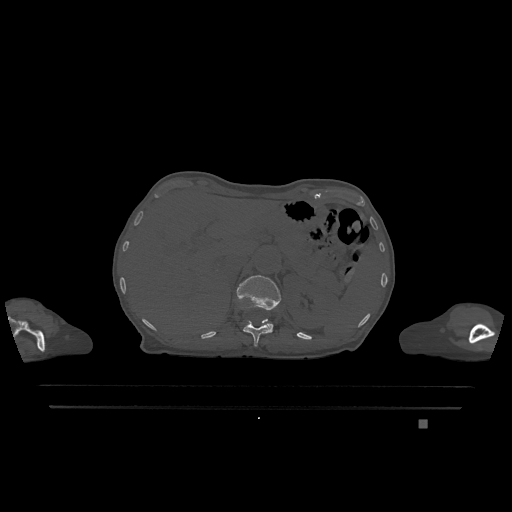
CT including the spine, one axial slice. Position 510 of 1317 along the scan axis. Bone window (W 1800 / L 400 HU). 0.5 mm slice thickness. 512 × 512 image matrix, field of view 500 × 500 mm. Patient: female, 74 years. Case-level facts recorded for this patient, not image findings: primary cancer: lung; vertebrae with lytic lesions (as recorded): T1, T4, T5, T6, L4, L5.
Structures marked on this image (semi-automatically segmented with operator editing):
- L1 vertebra: bounding box <237,275,281,332> (left, top, right, bottom; pixels)
- T12 vertebra: <243,319,271,346>